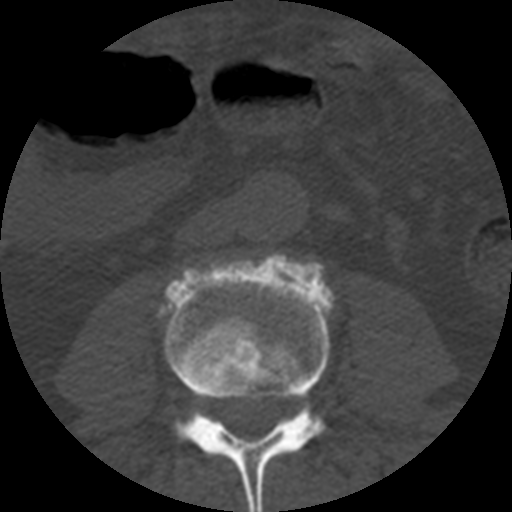
CT including the spine, one axial slice; position 117 of 508 along the scan axis; 120 kVp; bone window (W 1800 / L 400 HU); 512 × 512 image matrix, field of view 160 × 160 mm. Patient age 57 years. From the clinical record (not read from this slice): primary cancer: prostate.
Outlined on this slice (semi-automatically segmented with operator editing):
- L3 vertebra: bounding box <164,254,334,512> (left, top, right, bottom; pixels)